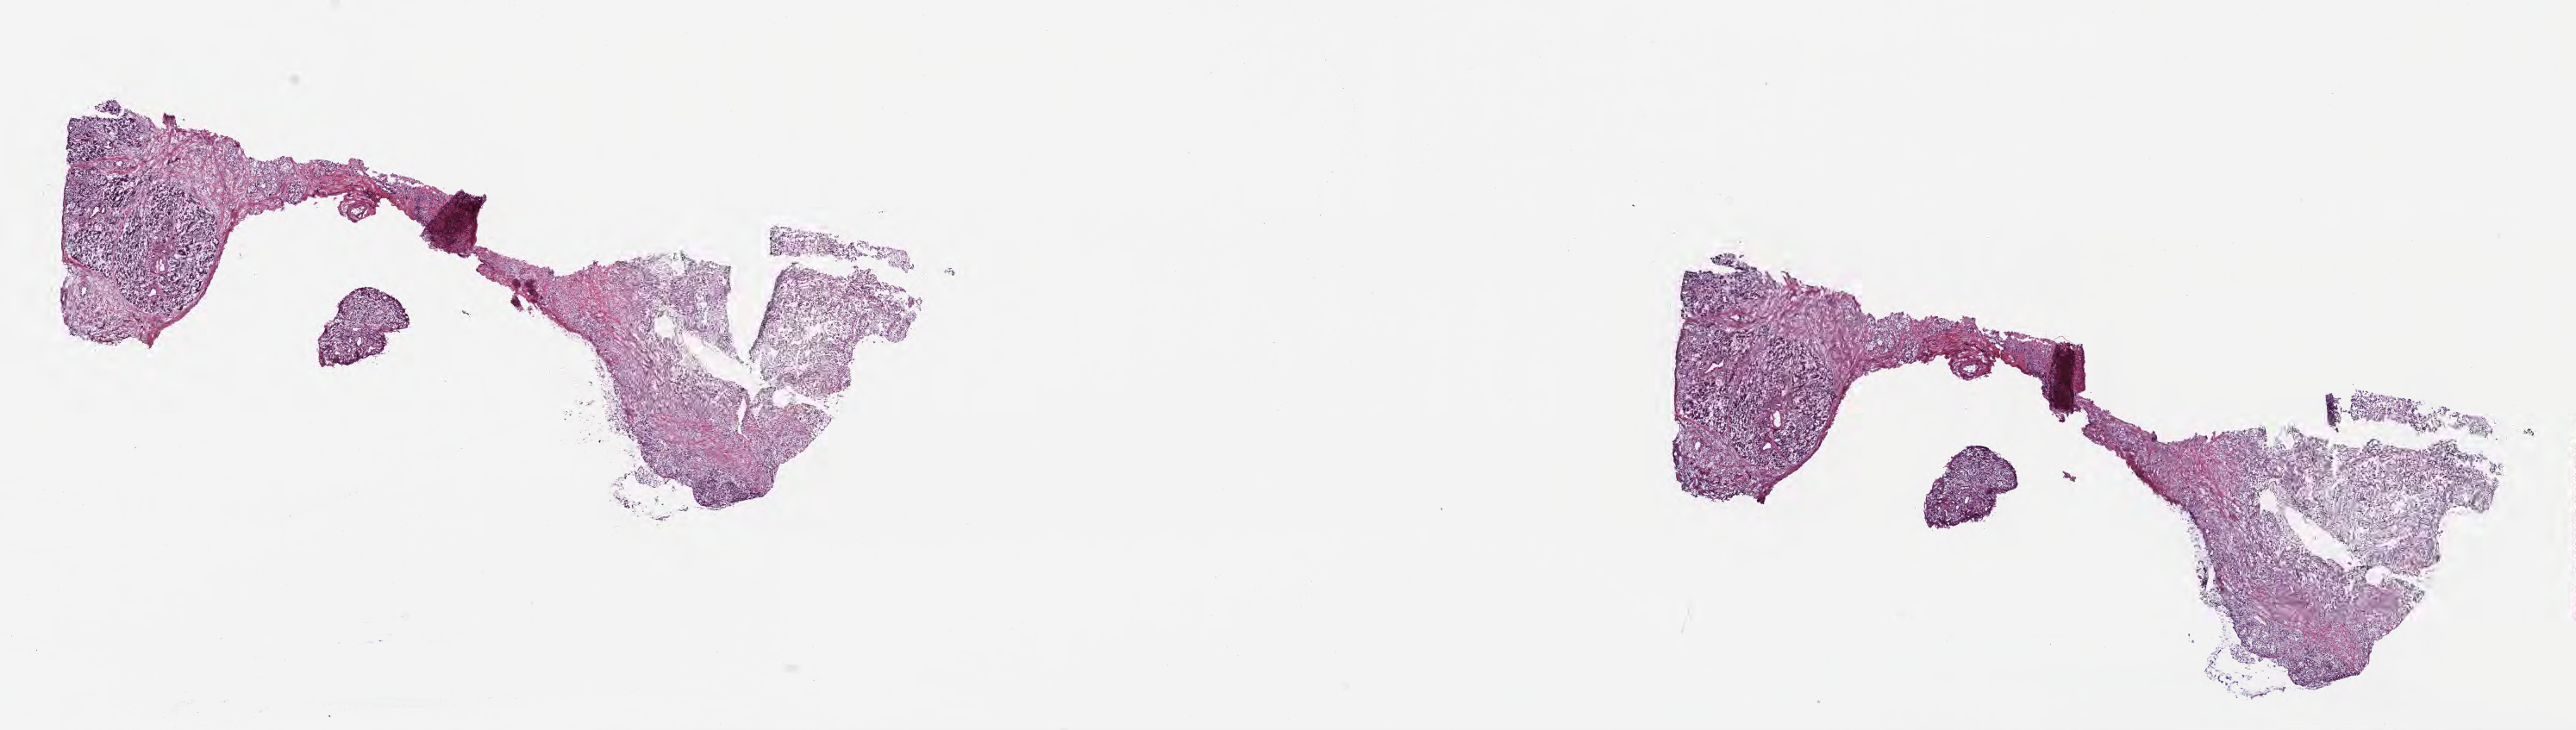
Haematoxylin and eosin whole-slide image — whole scanned area (about 24.1 x 6.8 mm) shown as a low-resolution overview, frozen section (tissue freezing medium), primary tumor, anatomic site: head of pancreas. Patient: male, age at initial diagnosis 57 years. Tumor grade: G2 (moderately differentiated). Slide review estimates, as recorded: tumor cells 24%, tumor nuclei 50%, stromal cells 42%, necrosis 2%, normal cells 32%. Inflammatory infiltration, as recorded: lymphocyte infiltration 20%, monocyte infiltration 4%, neutrophil infiltration 0%.
Diagnosis: Infiltrating duct carcinoma, NOS. AJCC pathologic stage: Stage III.